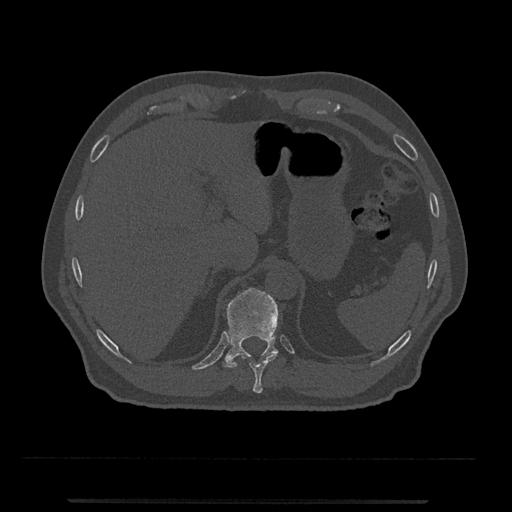
CT including the spine, one axial slice. Slice 487 of 797 in the series (ordered by position). Reconstruction kernel Br40s/3. 120 kVp. Bone window (W 1800 / L 400 HU). 0.5 mm slice thickness. 512 × 512 image matrix. Male patient, age 63 years. From the clinical record (not read from this slice): primary cancer: prostate.
Annotated regions visible in this slice (semi-automatically segmented with operator editing):
- T10 vertebra: box from (x=242, y=353) to (x=278, y=393) px
- T11 vertebra: (x=223, y=288)–(x=279, y=368)